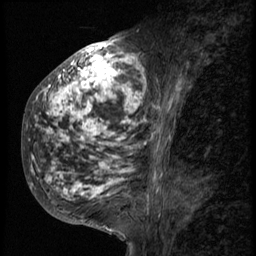
Breast MRI (dynamic contrast-enhanced), one sagittal slice; slice 27 of 58 in the series (ordered by position); 3 images stored at this slice position (order not interpretable as contrast timing); 1.5 T; TE 4.2 ms, TR 9 ms; 256 × 256 image matrix. Patient: female, 50 years. From the clinical record (not read from this slice): setting: breast cancer imaged before/during neoadjuvant chemotherapy; receptor status: triple-negative.
Structures marked on this image (semi-automatic segmentation, software-assisted and operator-edited):
- analysis volume of interest (the breast-tissue region the enhancement analysis was run in; not a lesion): bounding box [x1, y1, x2, y2] px = [23, 48, 158, 214]
- tumour enhancement mask (voxels above the 140 % enhancement threshold inside the analysis volume of interest): [31, 48, 158, 201]